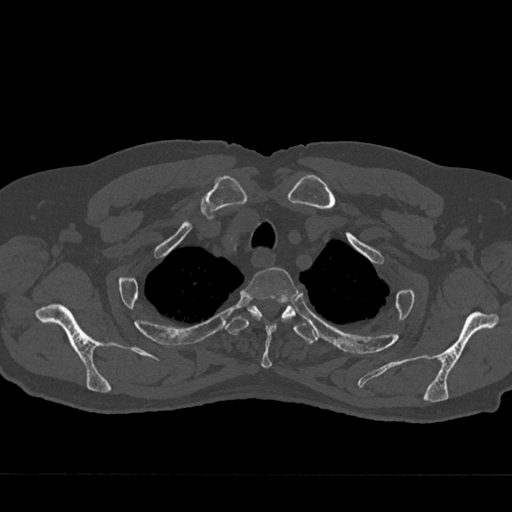
CT including the spine, one axial slice; position 591 of 797 along the scan axis; reconstruction kernel Br40s/3; bone window (W 1800 / L 400 HU); 512 × 512 image matrix, field of view 377 × 377 mm. Patient: male, 75 years. Case-level facts recorded for this patient, not image findings: primary cancer: renal.
Annotated regions visible in this slice (semi-automatically segmented with operator editing):
- T2 vertebra: bounding box [x1, y1, x2, y2] px = [243, 267, 298, 368]
- T3 vertebra: [226, 305, 318, 344]